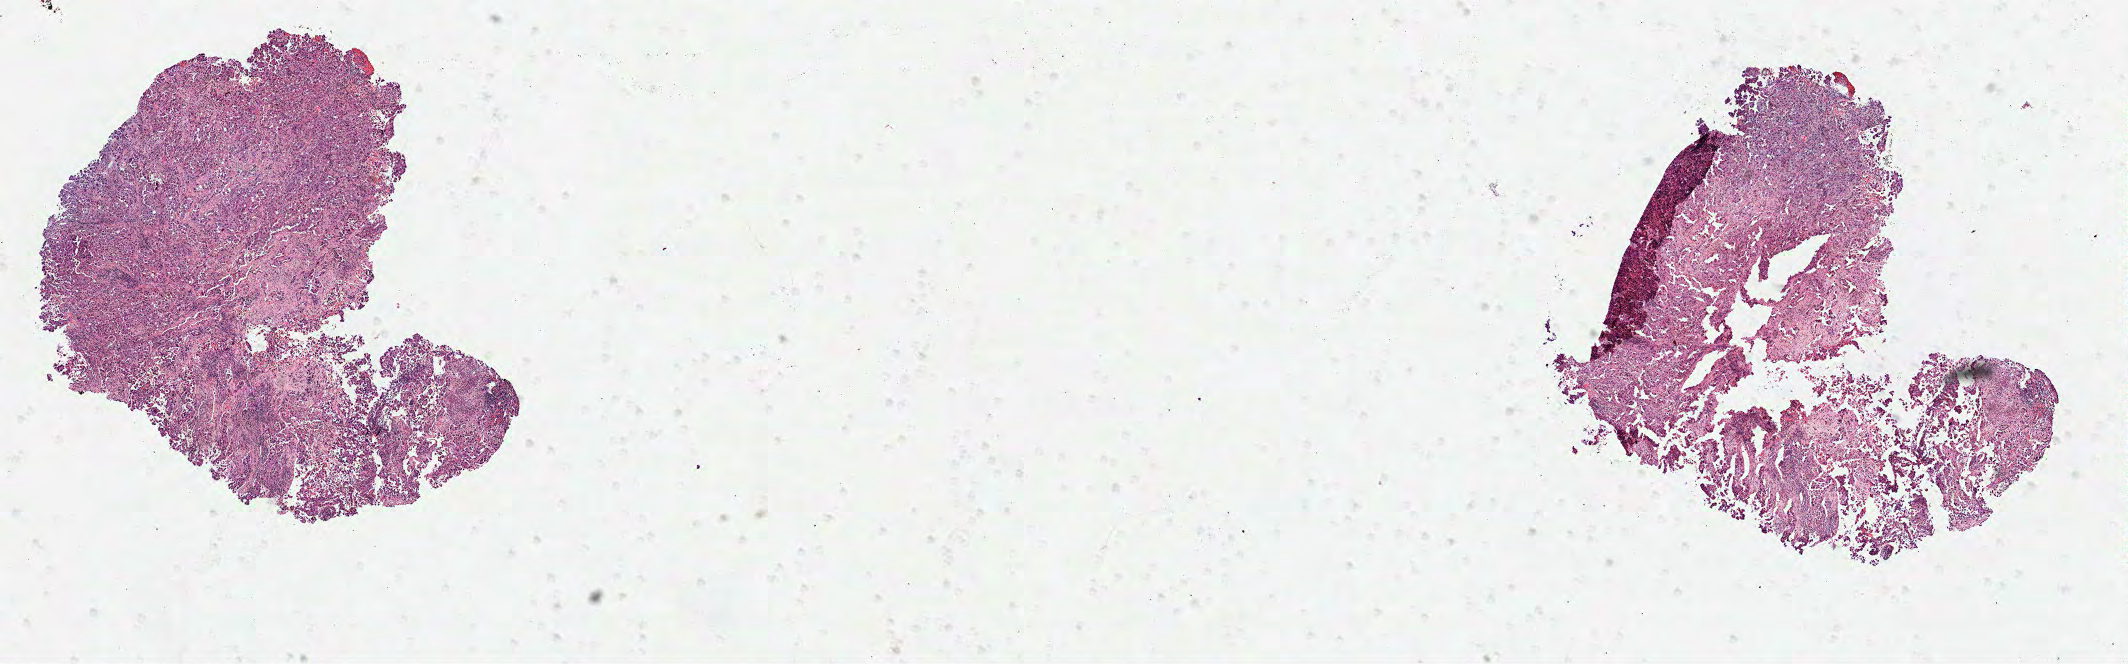
Digitized Hematoxylin and eosin (H&E) stained tissue section (whole slide) — low-resolution overview of the scanned area, about 17.2 x 5.4 mm (slide scanned at 40x), FFPE section, lung, primary tumour sample. Patient: male, age at initial diagnosis 61 years.
Diagnosis: Adenocarcinoma, NOS (upper lobe, lung). AJCC pathologic stage: IB.